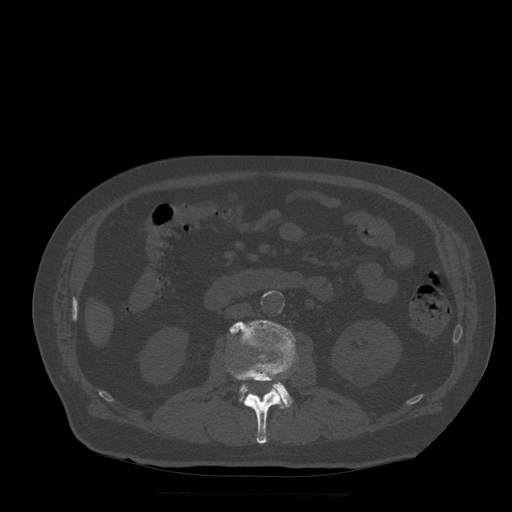
CT including the spine, one axial slice; position 158 of 522 along the scan axis; bone window (W 1800 / L 400 HU); 512 × 512 image matrix, field of view 420 × 420 mm. Patient age 72 years. From the clinical record (not read from this slice): primary cancer: prostate.
Outlined on this slice (semi-automatically segmented with operator editing):
- L2 vertebra: bounding box (x1, y1, x2, y2) in pixels: (228, 360, 286, 444)
- L3 vertebra: (230, 320, 296, 408)